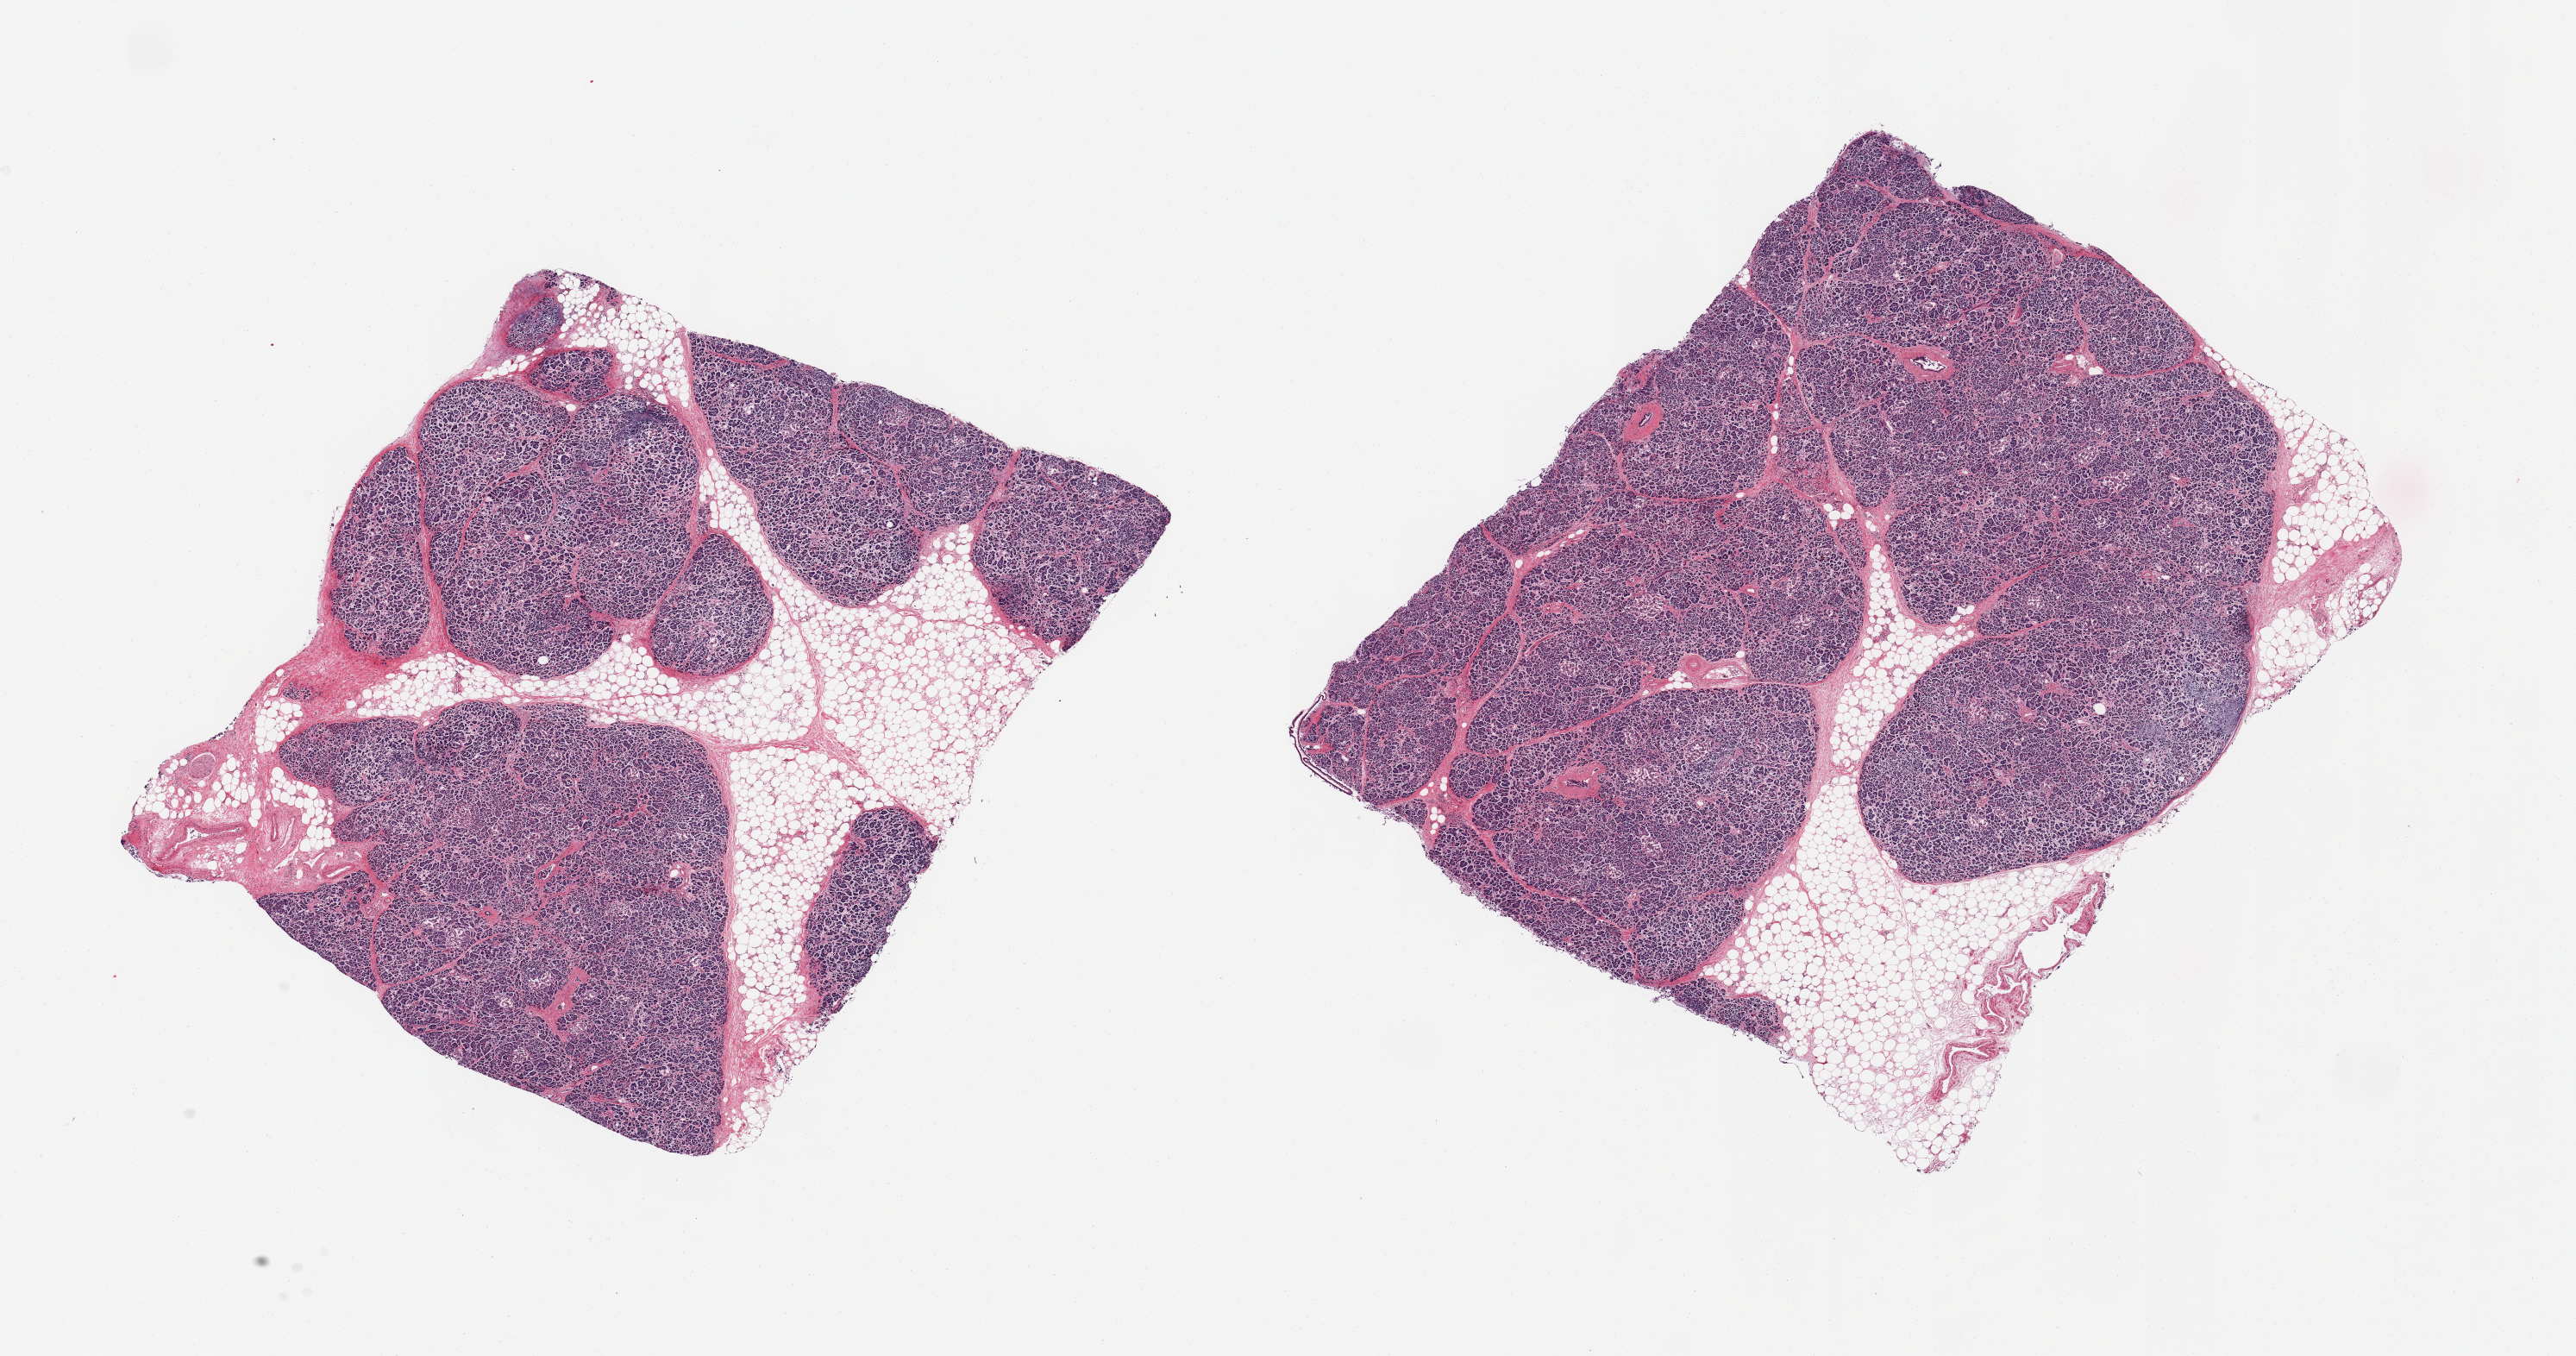
Whole-slide image, H&E stain, low-resolution overview of the scanned area, about 23.6 x 12.4 mm, PAXgene-fixed, paraffin-embedded tissue, sampled site (target tissue): pancreas, donor tissue sample.
Review note (as recorded): 2 pieces; includes 20-30% fat (attached and internal), some fibrosis.